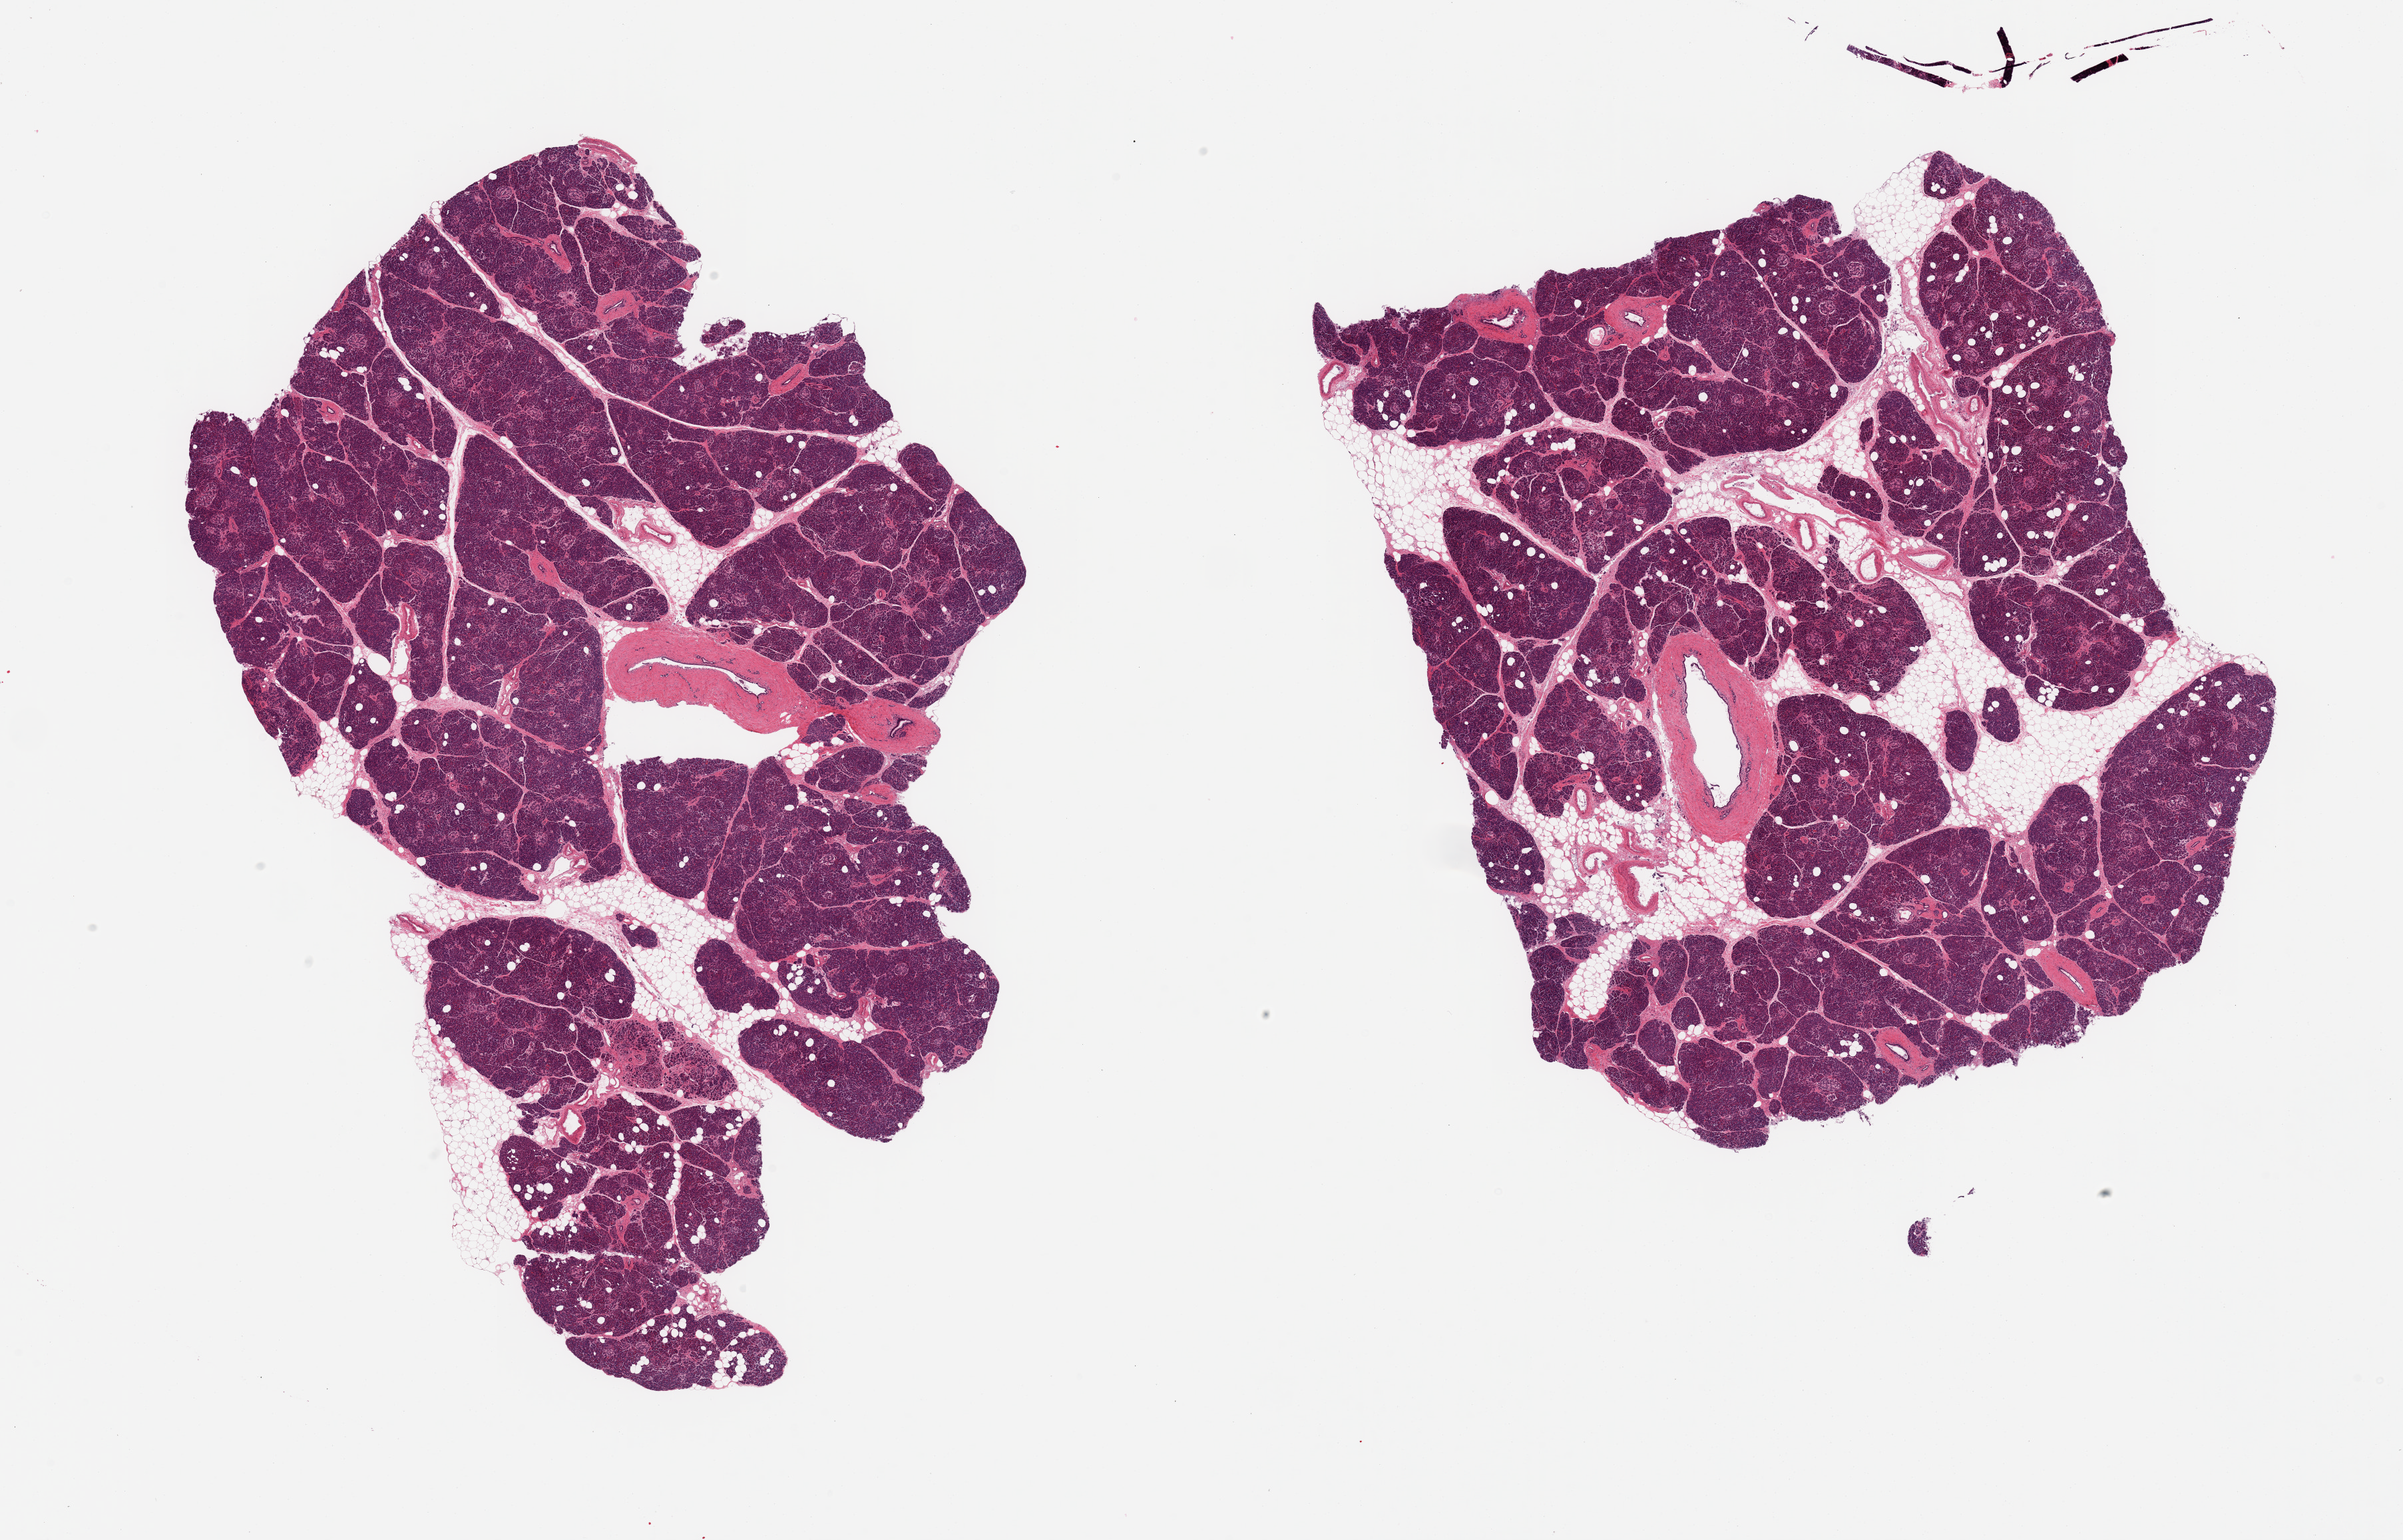
Digitized haematoxylin and eosin-stained section, shown as a low-resolution overview of the whole scanned area (about 28.5 x 18.3 mm). PAXgene-fixed, paraffin-embedded tissue. Target tissue: pancreas. Donor tissue sample. Donor sex: male.
* review note (as recorded): 2 pieces, abundant Islets, well-preserved